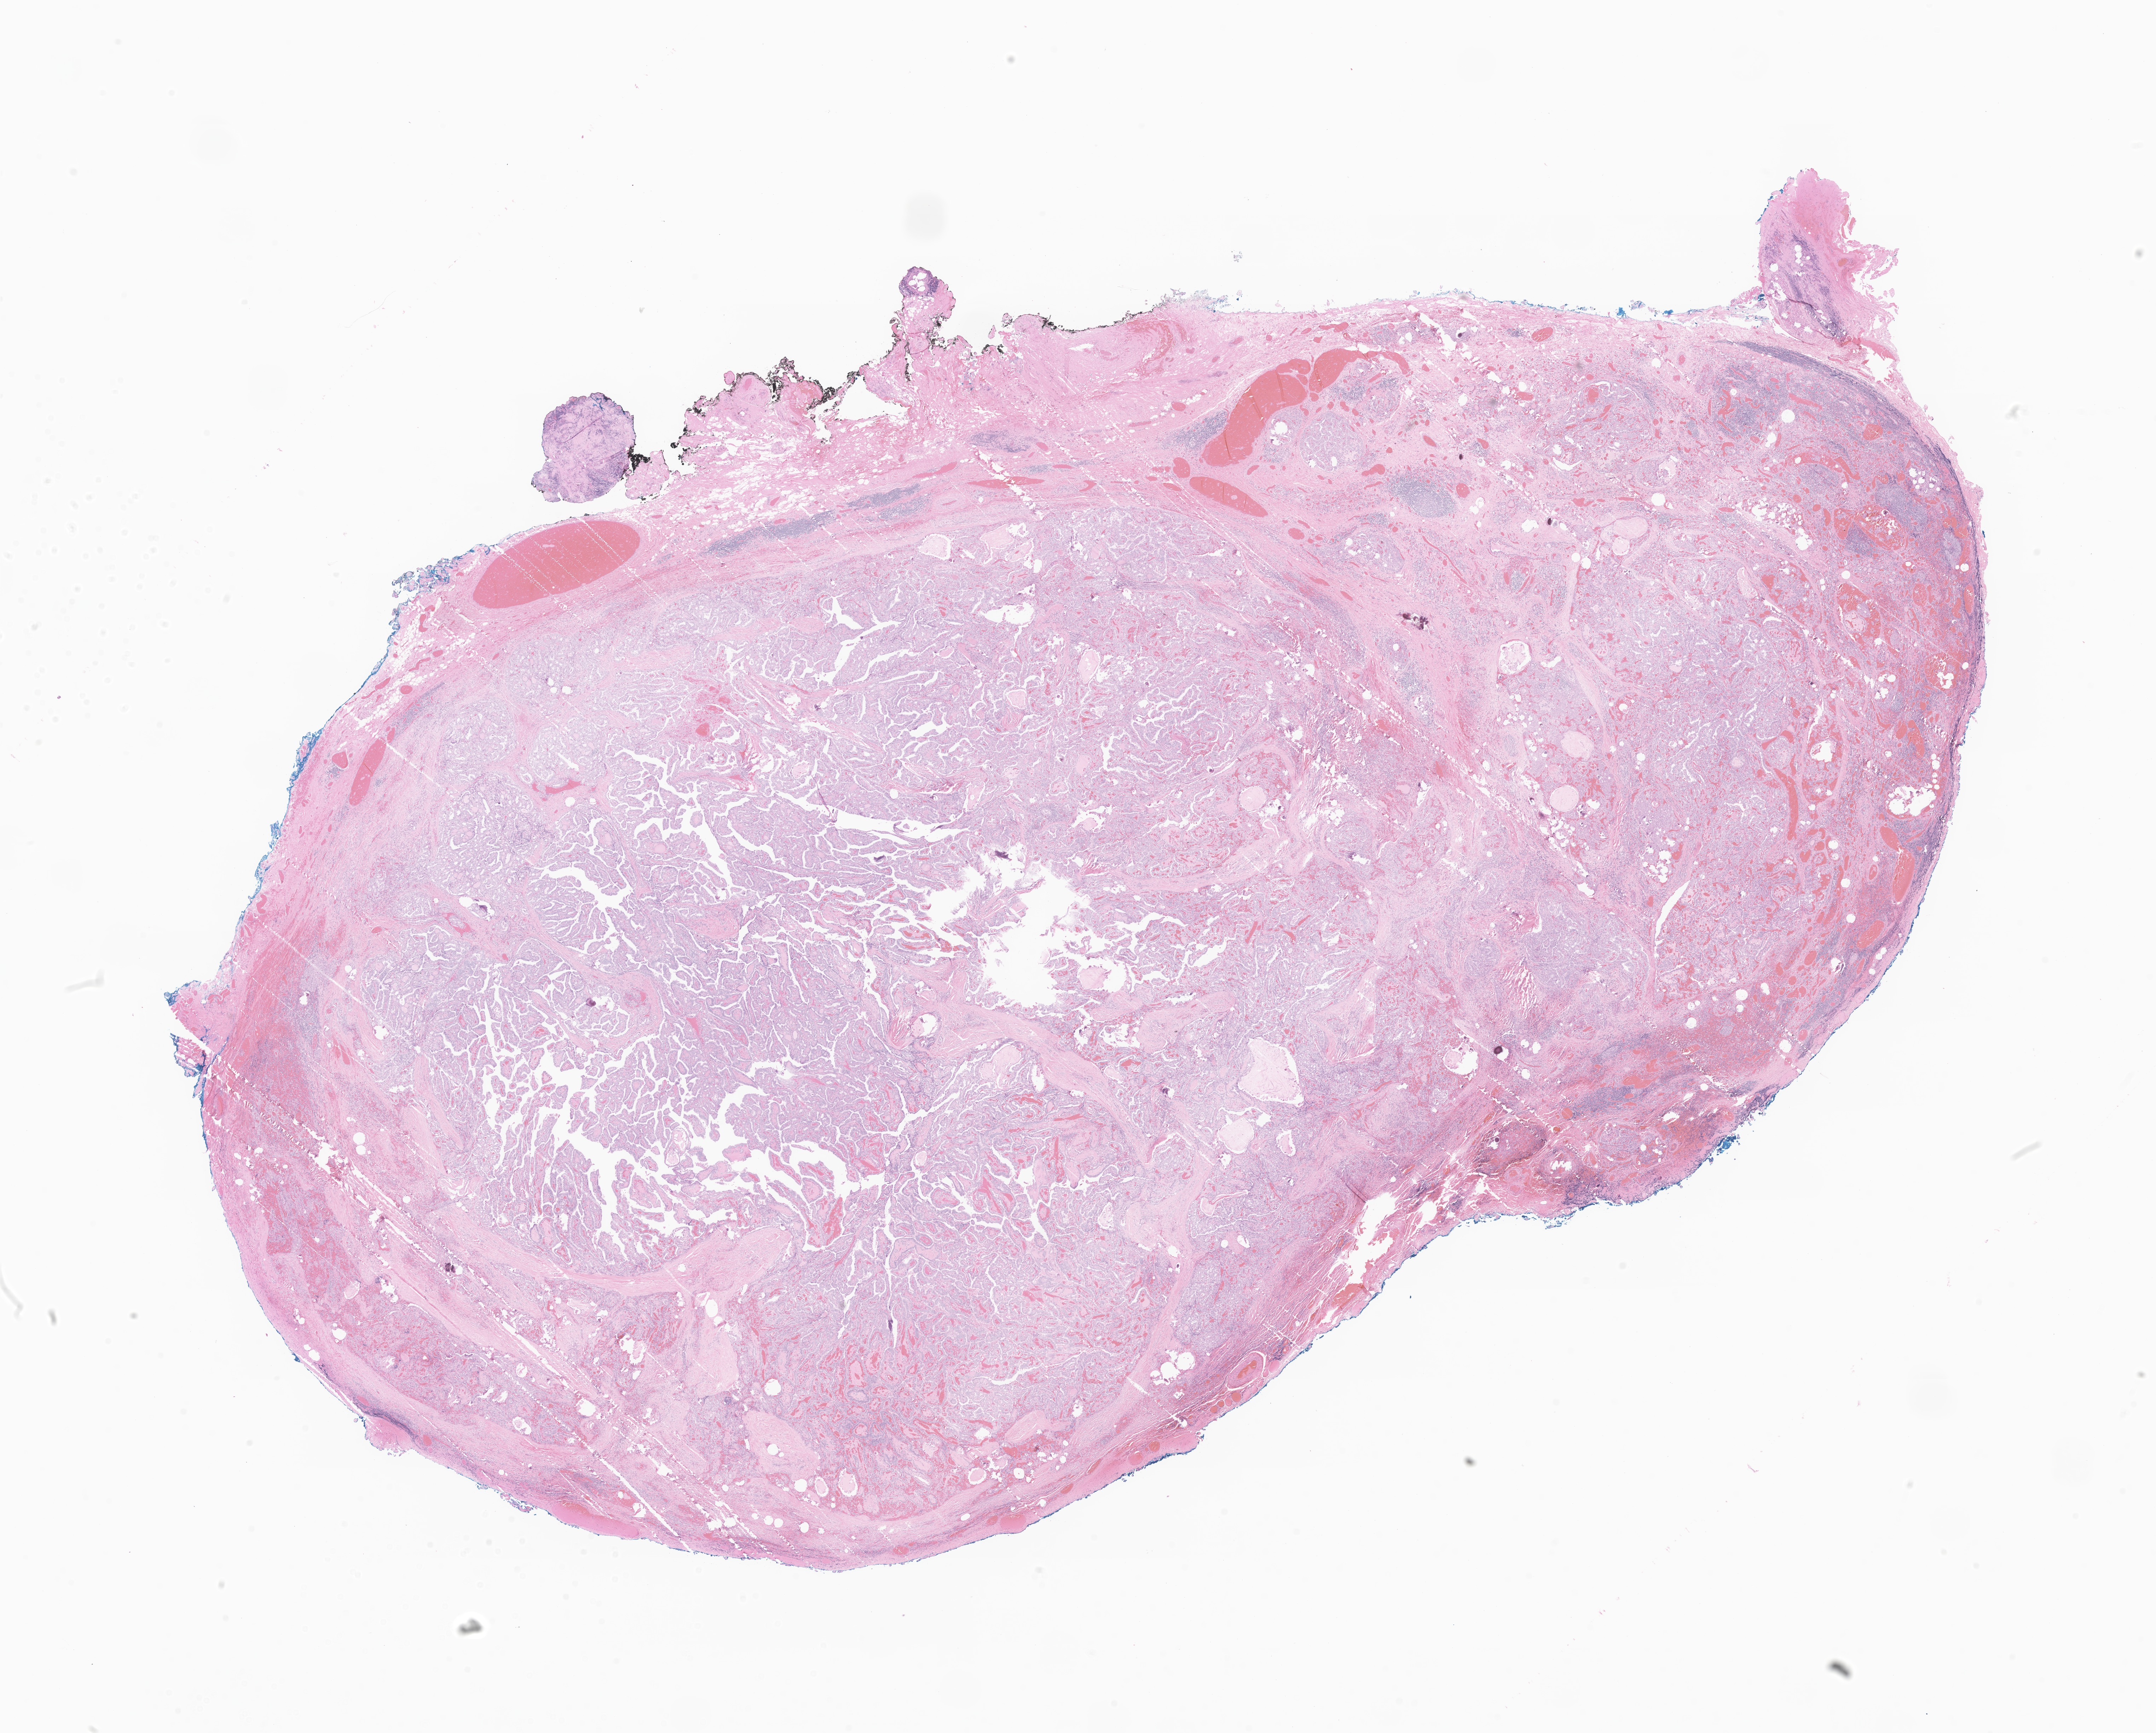
Whole-slide image, hematoxylin and eosin (H&E) stain of tumor tissue from the thyroid, low-resolution overview of the scanned area, about 25.7 x 20.7 mm; formalin-fixed paraffin-embedded section. Female patient, age 168 months (14 years).
• recorded diagnosis: Carcinoma, NOS